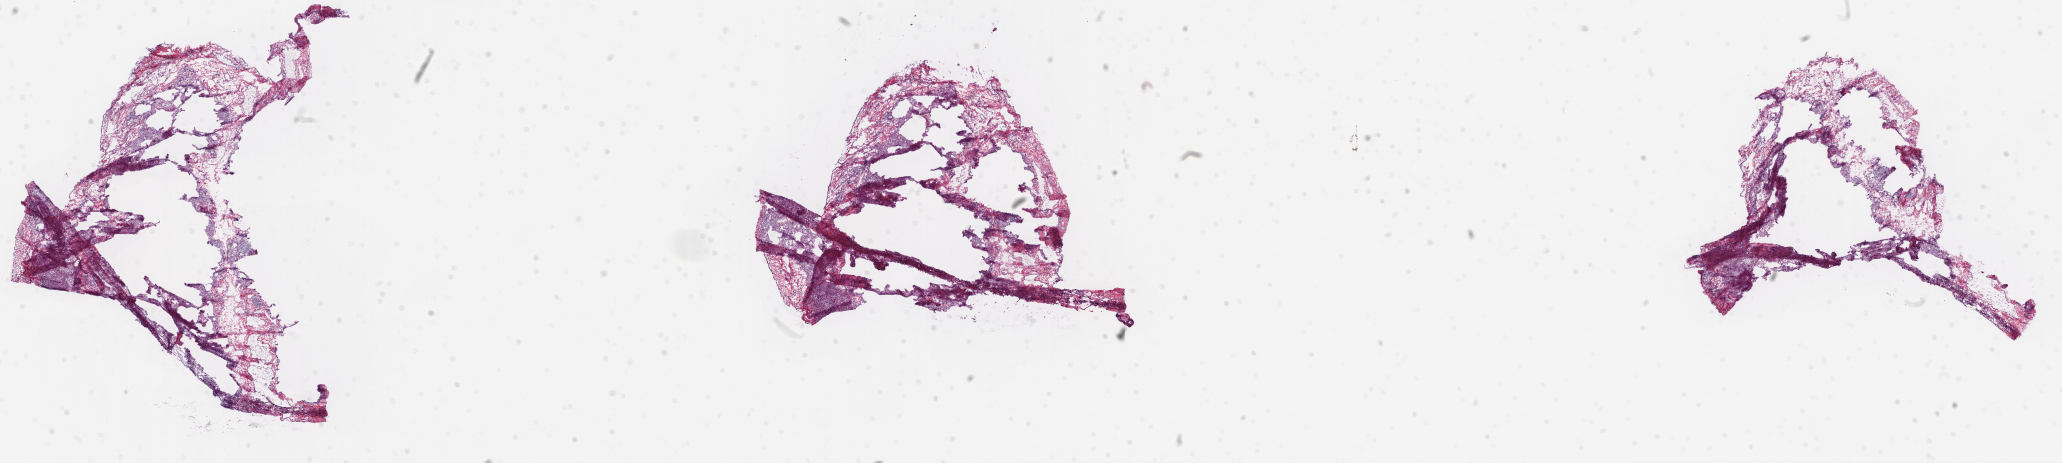
Whole-slide histology image, H&E, whole scanned area (about 33.1 x 7.4 mm) shown as a low-resolution overview, frozen section from the top of the tissue portion, solid tissue normal (non-tumour tissue) sample from the lung. Male, age 54 years at initial diagnosis.
• this section: solid tissue normal sample (biorepository sample class)
• patient diagnosis: Squamous cell carcinoma, NOS (upper lobe, lung)